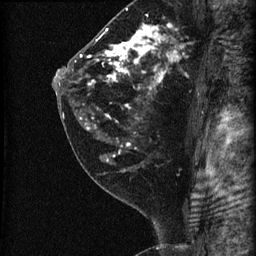
Breast MRI (dynamic contrast-enhanced), one sagittal slice. Slice 40 of 60 in the series (ordered by position). Dynamic contrast-enhanced series, image 2 of 3 at this slice position (ordered by acquisition). 1.5 T. TE 4.2 ms, TR 22.7 ms. 256 × 256 image matrix, field of view 180 × 180 mm. Patient: female, 45 years. Case-level facts recorded for this patient, not image findings: setting: breast cancer imaged before/during neoadjuvant chemotherapy; receptor status: HR-positive, HER2-negative.
Outlined on this slice (semi-automatically segmented with operator editing):
- analysis volume of interest (the breast-tissue region the enhancement analysis was run in; not a lesion): bounding box <74,11,205,140> (left, top, right, bottom; pixels)
- tumour enhancement mask (voxels above the 90 % enhancement threshold inside the analysis volume of interest): <80,23,178,129>